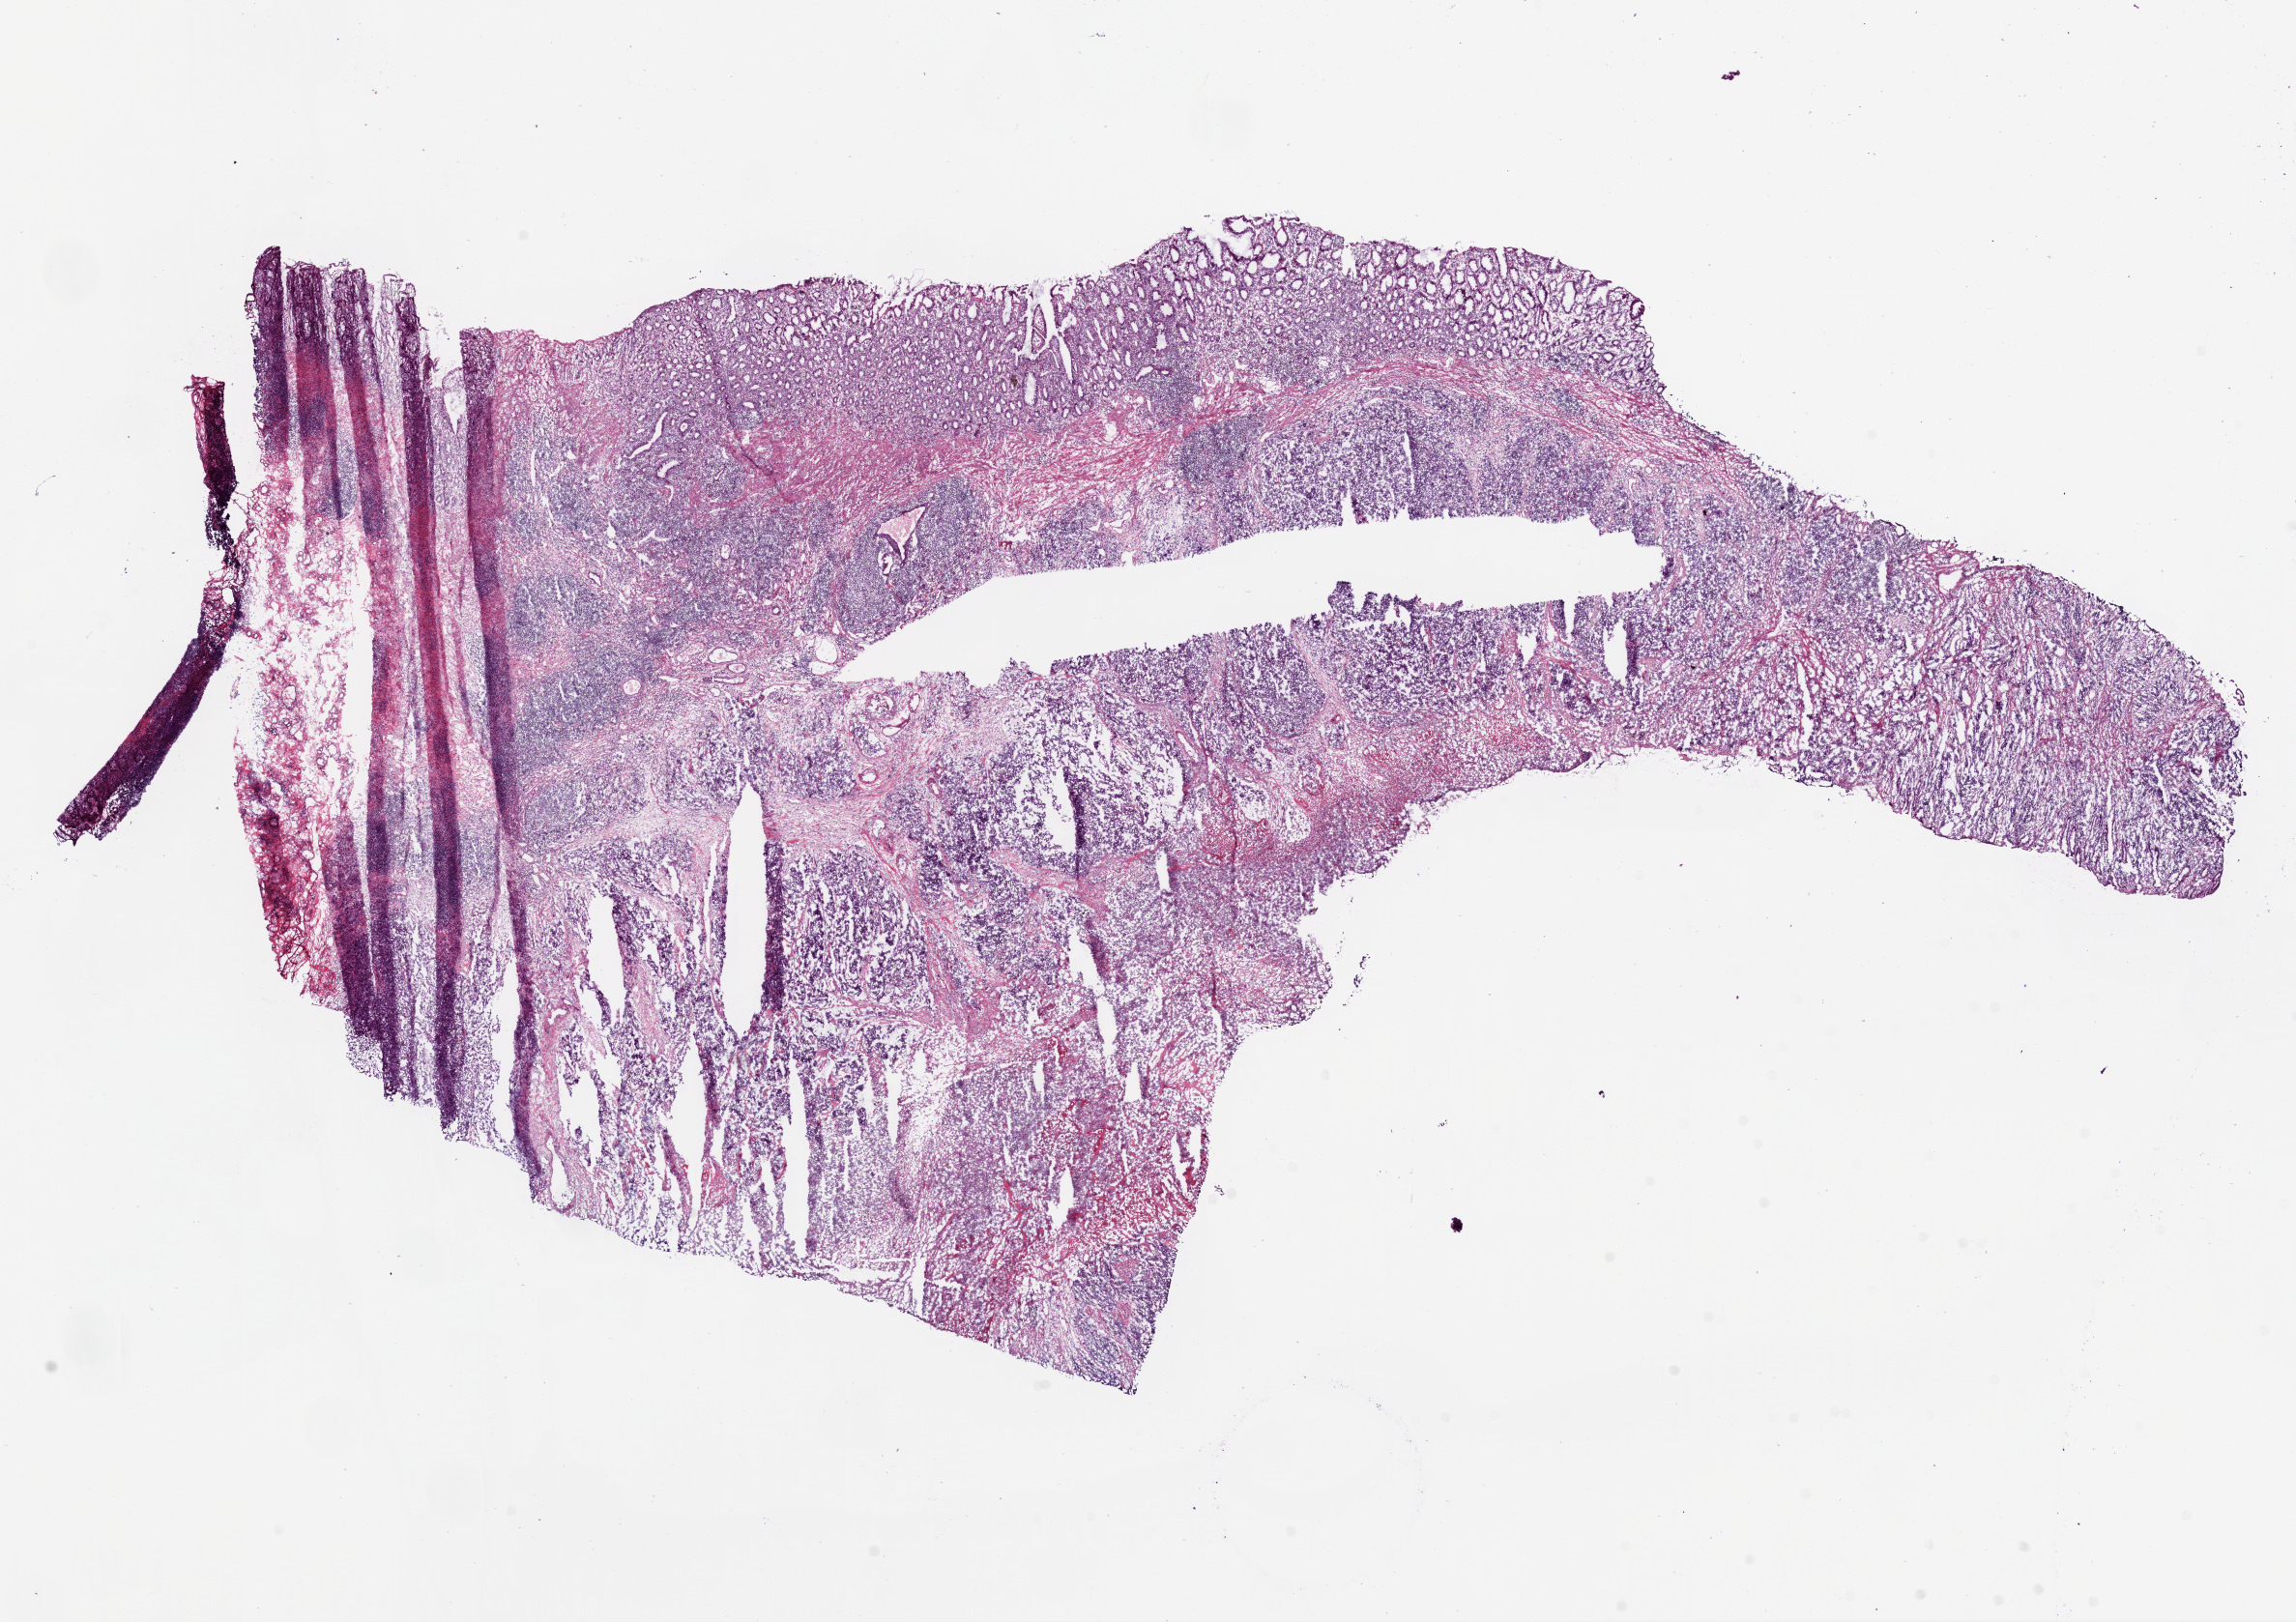
Digitized H&E-stained tissue section (whole slide) — low-resolution overview of the scanned area, about 19.1 x 13.5 mm (from a 20x scan), frozen section, colon, primary tumour sample. Male patient; age at initial diagnosis 37 years. Composition of this section per pathologist review: tumour cells 65%, tumour nuclei 70%, normal cells 20%, stromal cells 10%, necrosis 5%.
Lymph nodes positive (case pathology): 5 of 30 examined. AJCC pathologic stage: IV. Pathologic diagnosis: Adenocarcinoma, NOS (cecum).